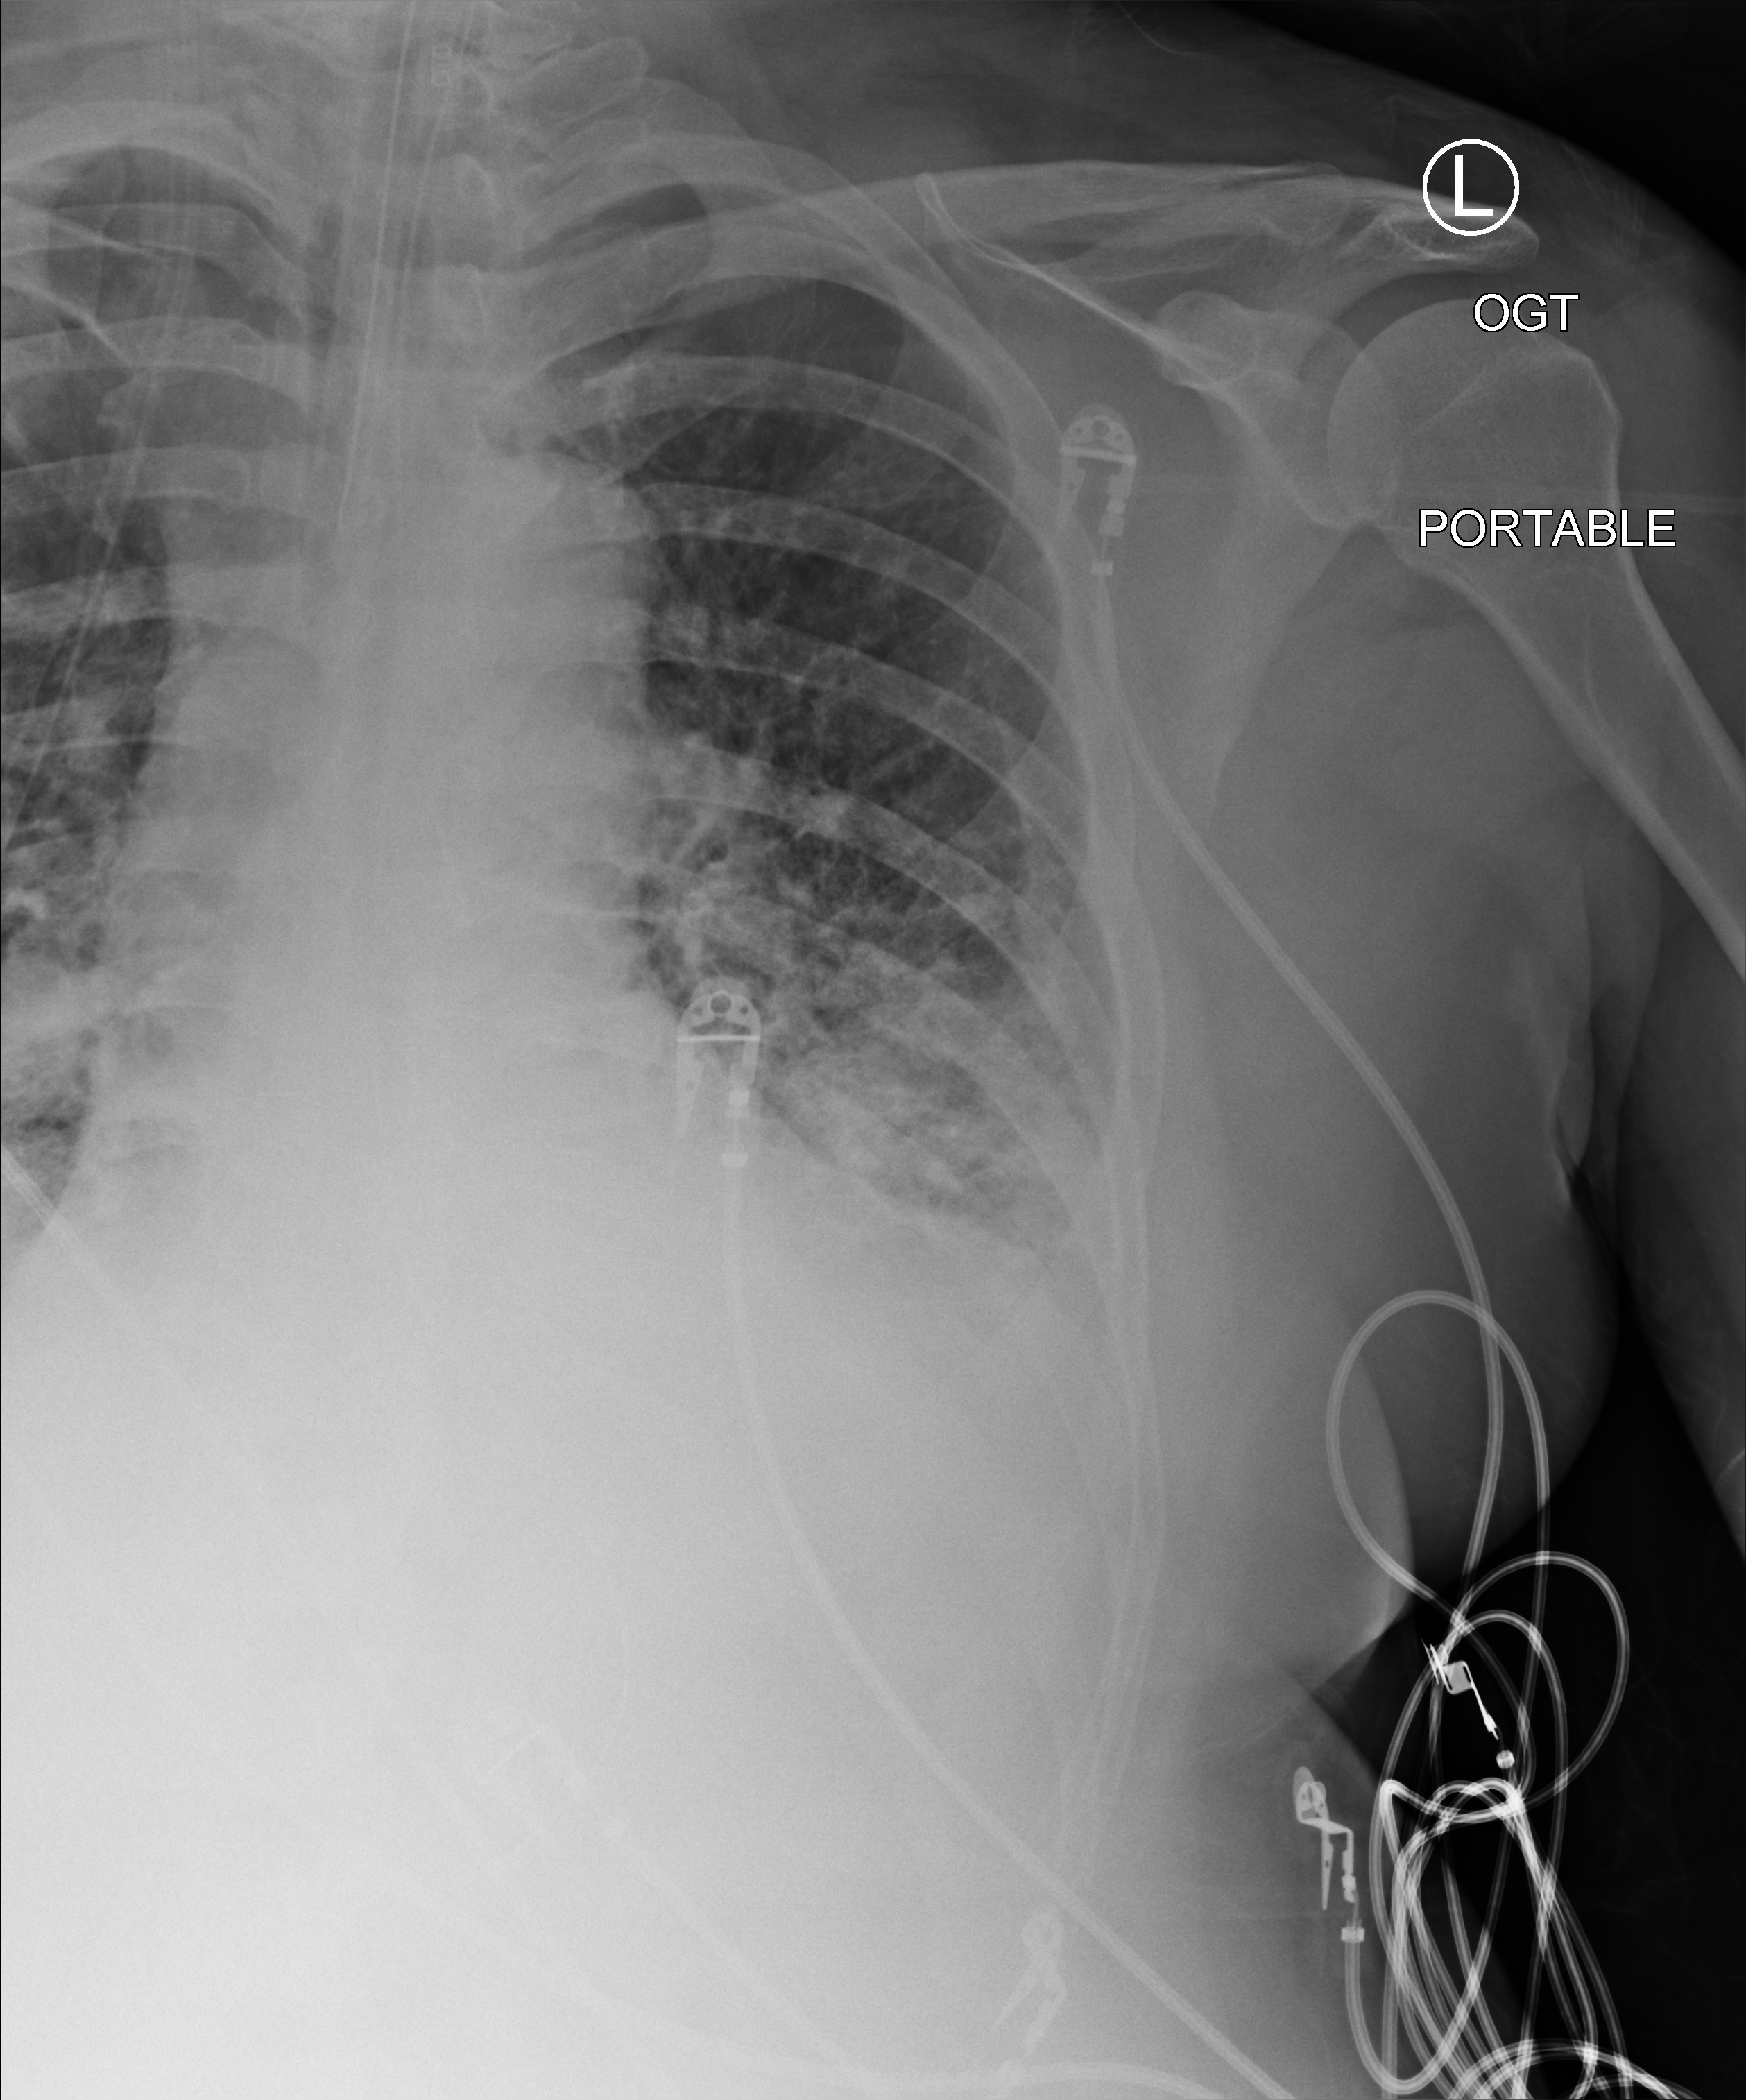
Chest X-ray (portable), anteroposterior (AP) projection. Adult patient hospitalised with COVID-19, age 18–59 years.
Hospital-stay facts (about this admission, not read from this image; timing relative to this image not recorded):
- hypertension (admission record): no
- admitted to intensive care during this hospital stay: yes